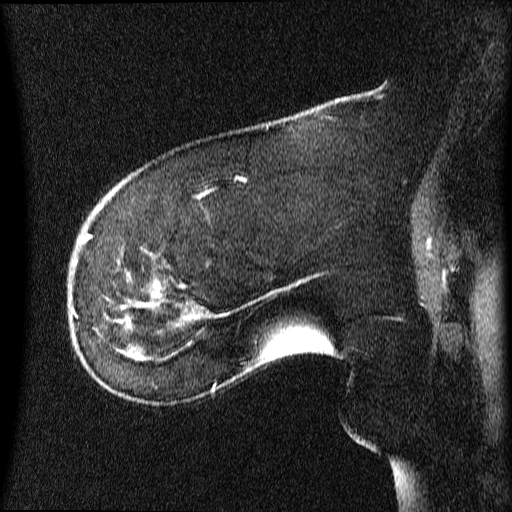
Breast MRI (dynamic contrast-enhanced), one sagittal slice; position 20 of 64 along the scan axis; dynamic contrast-enhanced series, image 2 of 4 at this slice position (ordered by acquisition); 1.5 T; TE 4.2 ms, TR 9 ms; 2 mm slice thickness; 512 × 512 image matrix, field of view 200 × 200 mm. Female patient, age 63 years.
Annotated regions visible in this slice (semi-automatically segmented with operator editing):
- analysis volume of interest (the breast-tissue region the enhancement analysis was run in; not a lesion): bounding box <70,272,131,353> (left, top, right, bottom; pixels)
- tumour enhancement mask (voxels above the 70 % enhancement threshold inside the analysis volume of interest): <120,306,126,353>